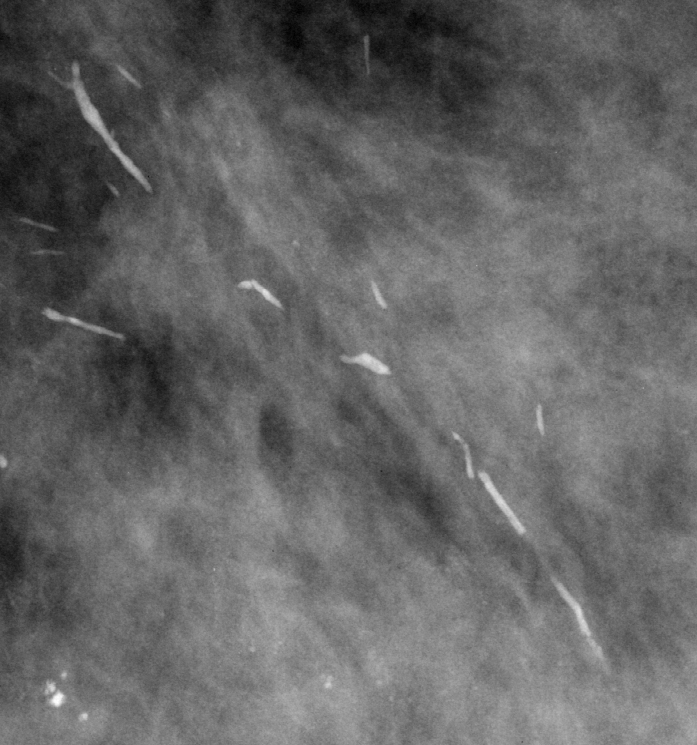
Crop from a digitized film mammogram around one marked abnormality; left breast; MLO view; BI-RADS breast density category 4 (scale 1–4).
Calcifications, morphology punctate / lucent center, distribution regional; BI-RADS assessment category 2; benign without callback (not worked up further).